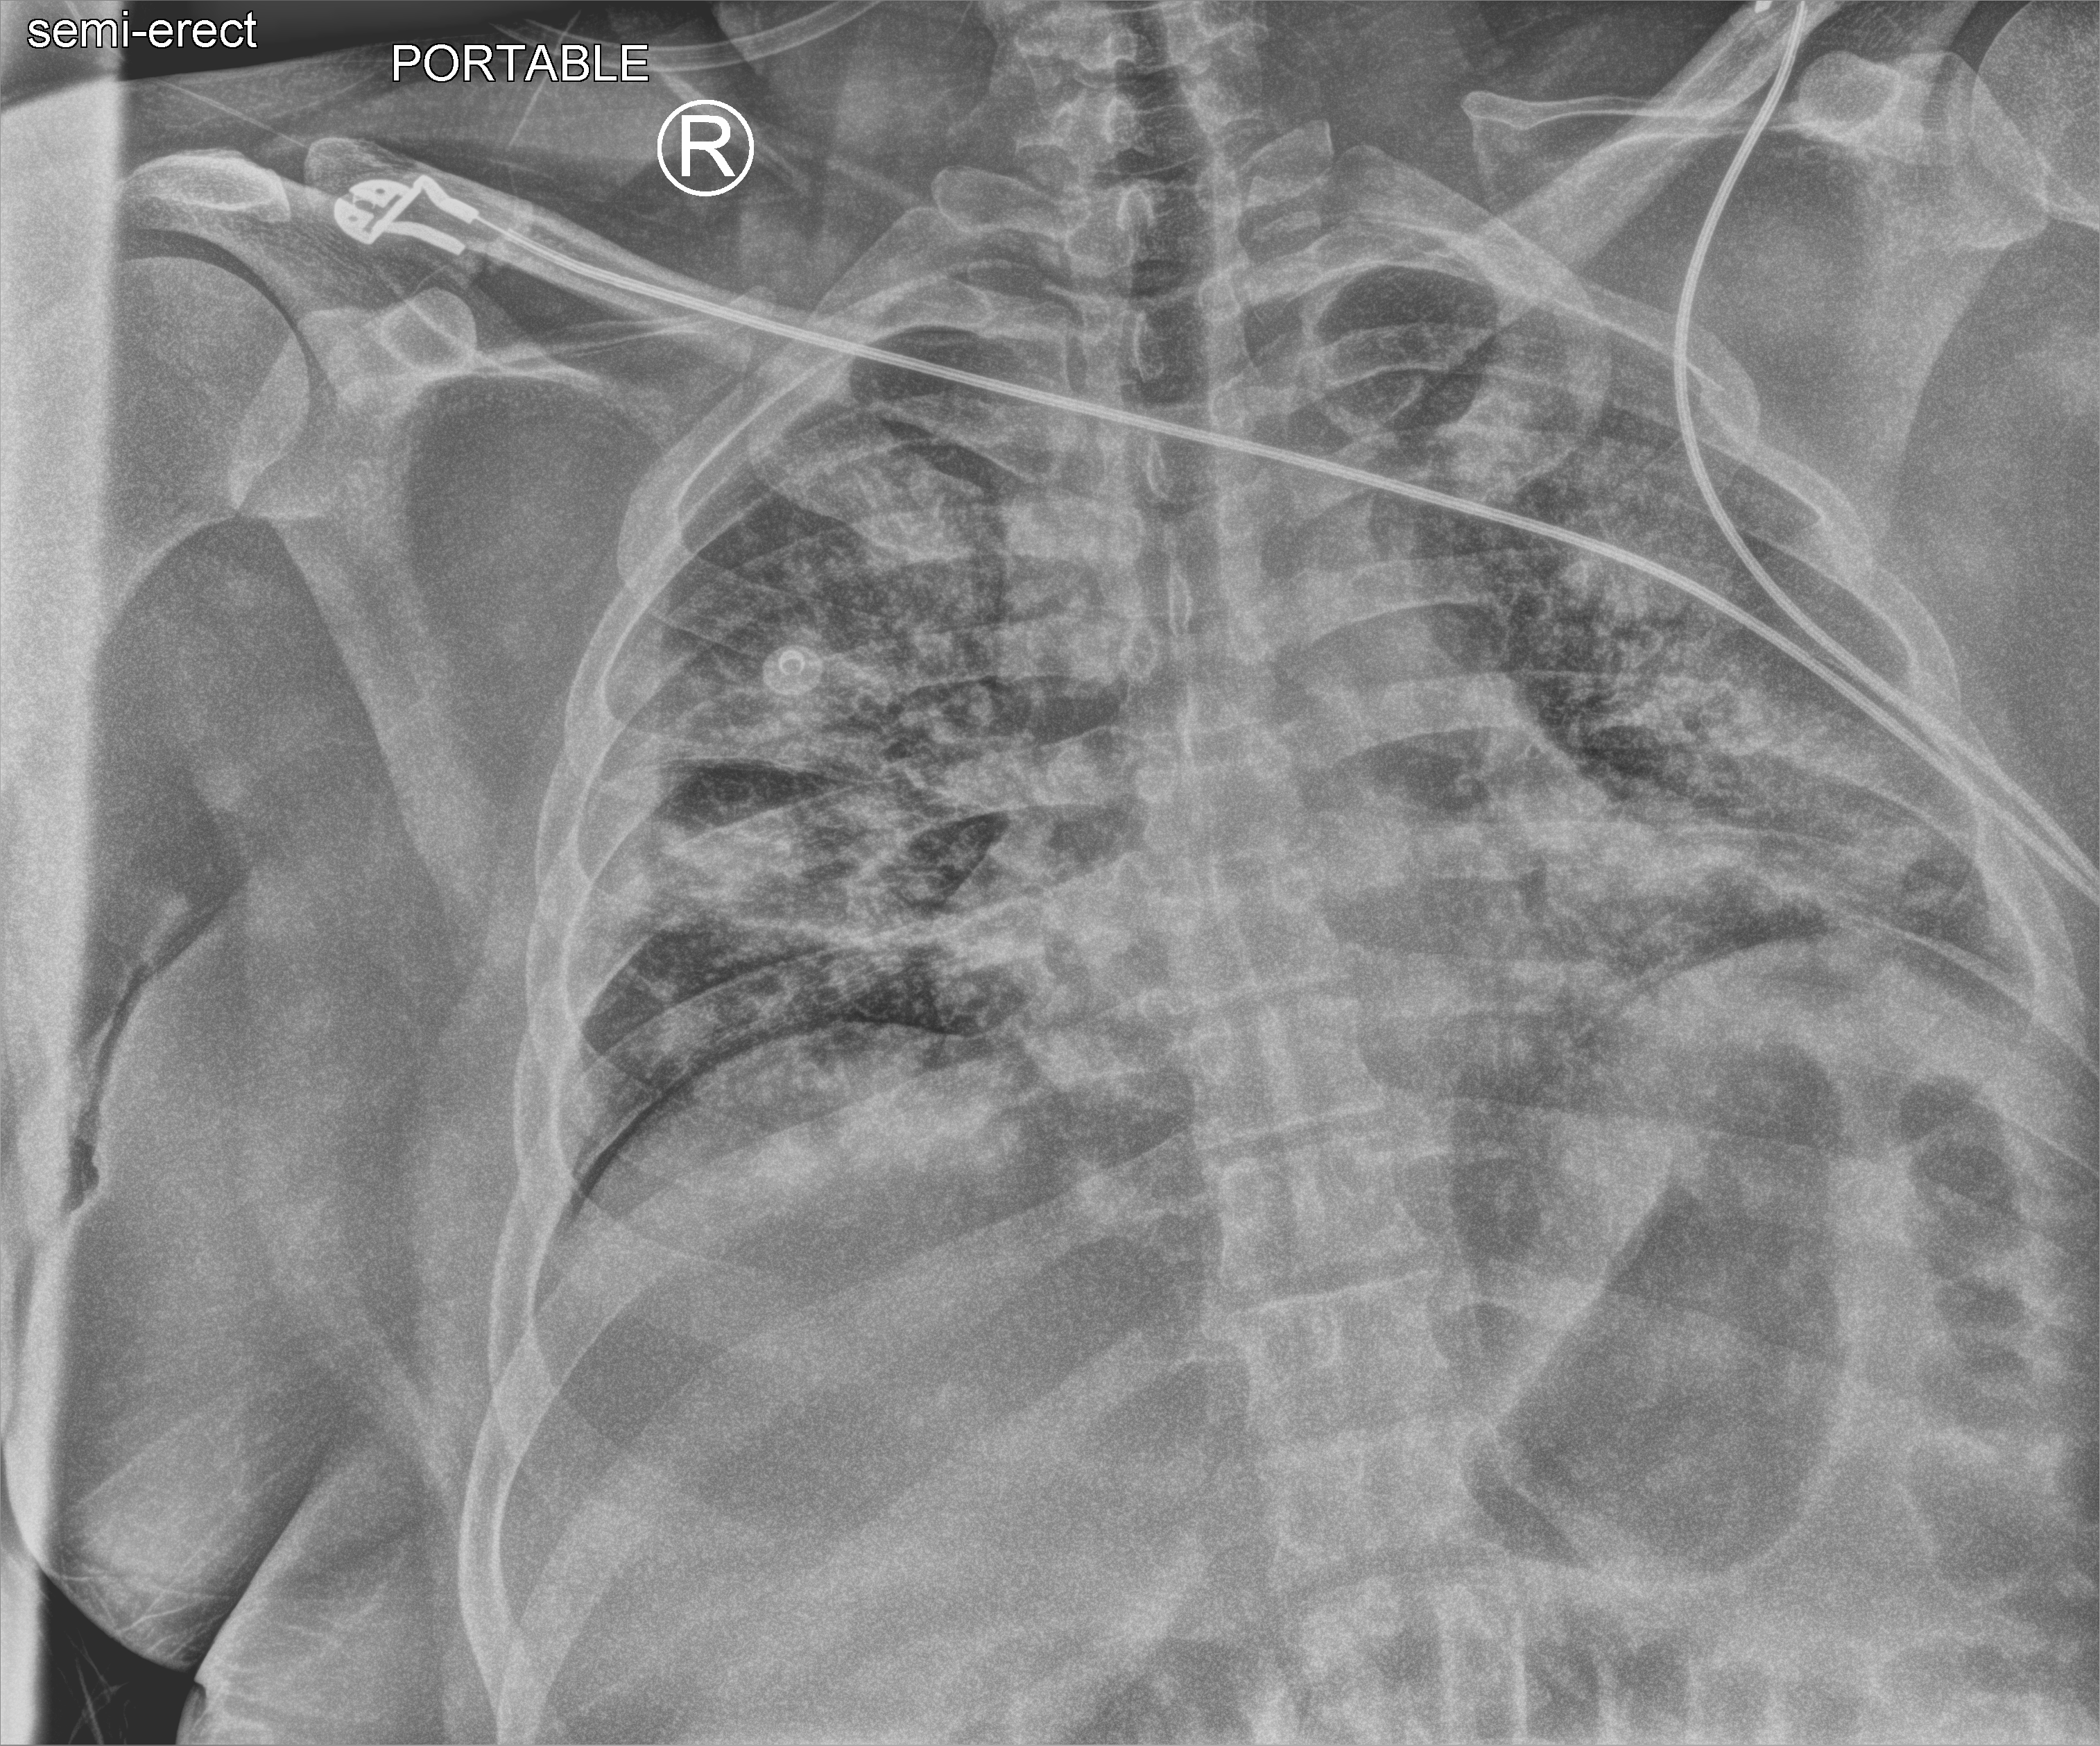
Chest X-ray (portable), anteroposterior (AP) projection. Adult patient hospitalised with COVID-19, age 18–59 years.
Admission-level facts for this patient (not findings on this image; timing relative to this image not recorded):
- diabetes (admission record): no
- admitted to intensive care during this hospital stay: yes